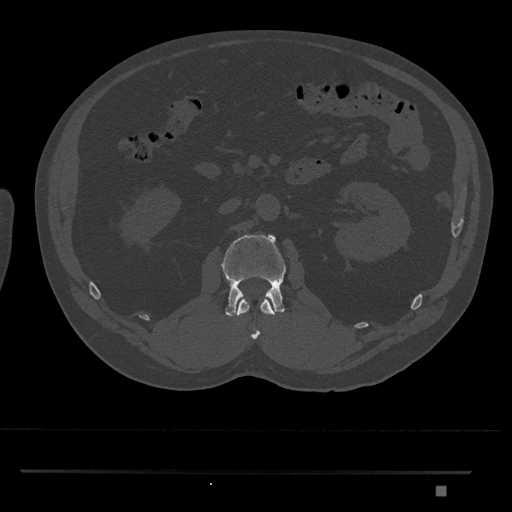
CT including the spine, one axial slice. Position 778 of 1134 along the scan axis. 120 kVp. Bone window (W 1800 / L 400 HU). 0.5 mm slice thickness. 512 × 512 image matrix, field of view 429 × 429 mm. Patient: male, 65 years. Case-level facts recorded for this patient, not image findings: primary cancer: prostate.
Annotated regions visible in this slice (semi-automatic segmentation, software-assisted and operator-edited):
- L1 vertebra: bounding box [x1, y1, x2, y2] px = [236, 298, 275, 340]
- L2 vertebra: [222, 234, 286, 317]